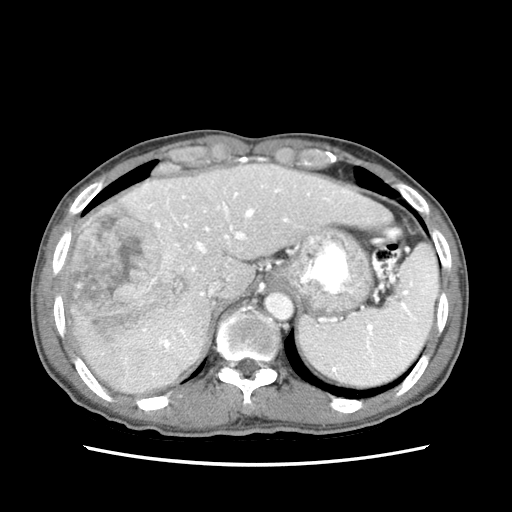
Contrast-enhanced abdominal CT (liver protocol), one axial slice; slice 55 of 79 in the series (ordered by position); soft-tissue window (W 400 / L 40 HU); 2.5 mm slice thickness; 512 × 512 image matrix, field of view 320 × 320 mm. From the clinical record (not read from this slice): diagnosis: hepatocellular carcinoma (patient treated with transarterial chemoembolisation; whether this scan precedes or follows treatment is not stated here); TNM stage (as recorded): Stage-IIIB; Child-Pugh class: A; tumour differentiation: moderately differentiated; tumour nodularity: multinodular.
Annotated regions visible in this slice (semi-automatic segmentation, software-assisted and operator-edited):
- abdominal aorta: box from (x=265, y=291) to (x=293, y=320) px
- liver parenchyma outside the tumour (the mass and vessels are separate outlines, so this box may not span the whole liver): (x=60, y=163)–(x=394, y=394)
- mass: (x=62, y=199)–(x=189, y=342)
- liver vessels: (x=120, y=177)–(x=330, y=349)